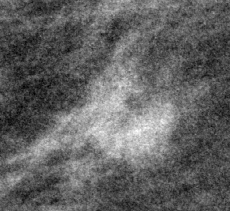
Cropped region of a digitized screen-film mammogram centred on a radiologist-marked abnormality; right breast; MLO view; BI-RADS breast density category 1 (scale 1–4).
- Finding: mass, shape lymph node, margins circumscribed; BI-RADS assessment category 2; subtlety rating 4 on a 1 (subtle) to 5 (obvious) scale; benign without callback (not worked up further).